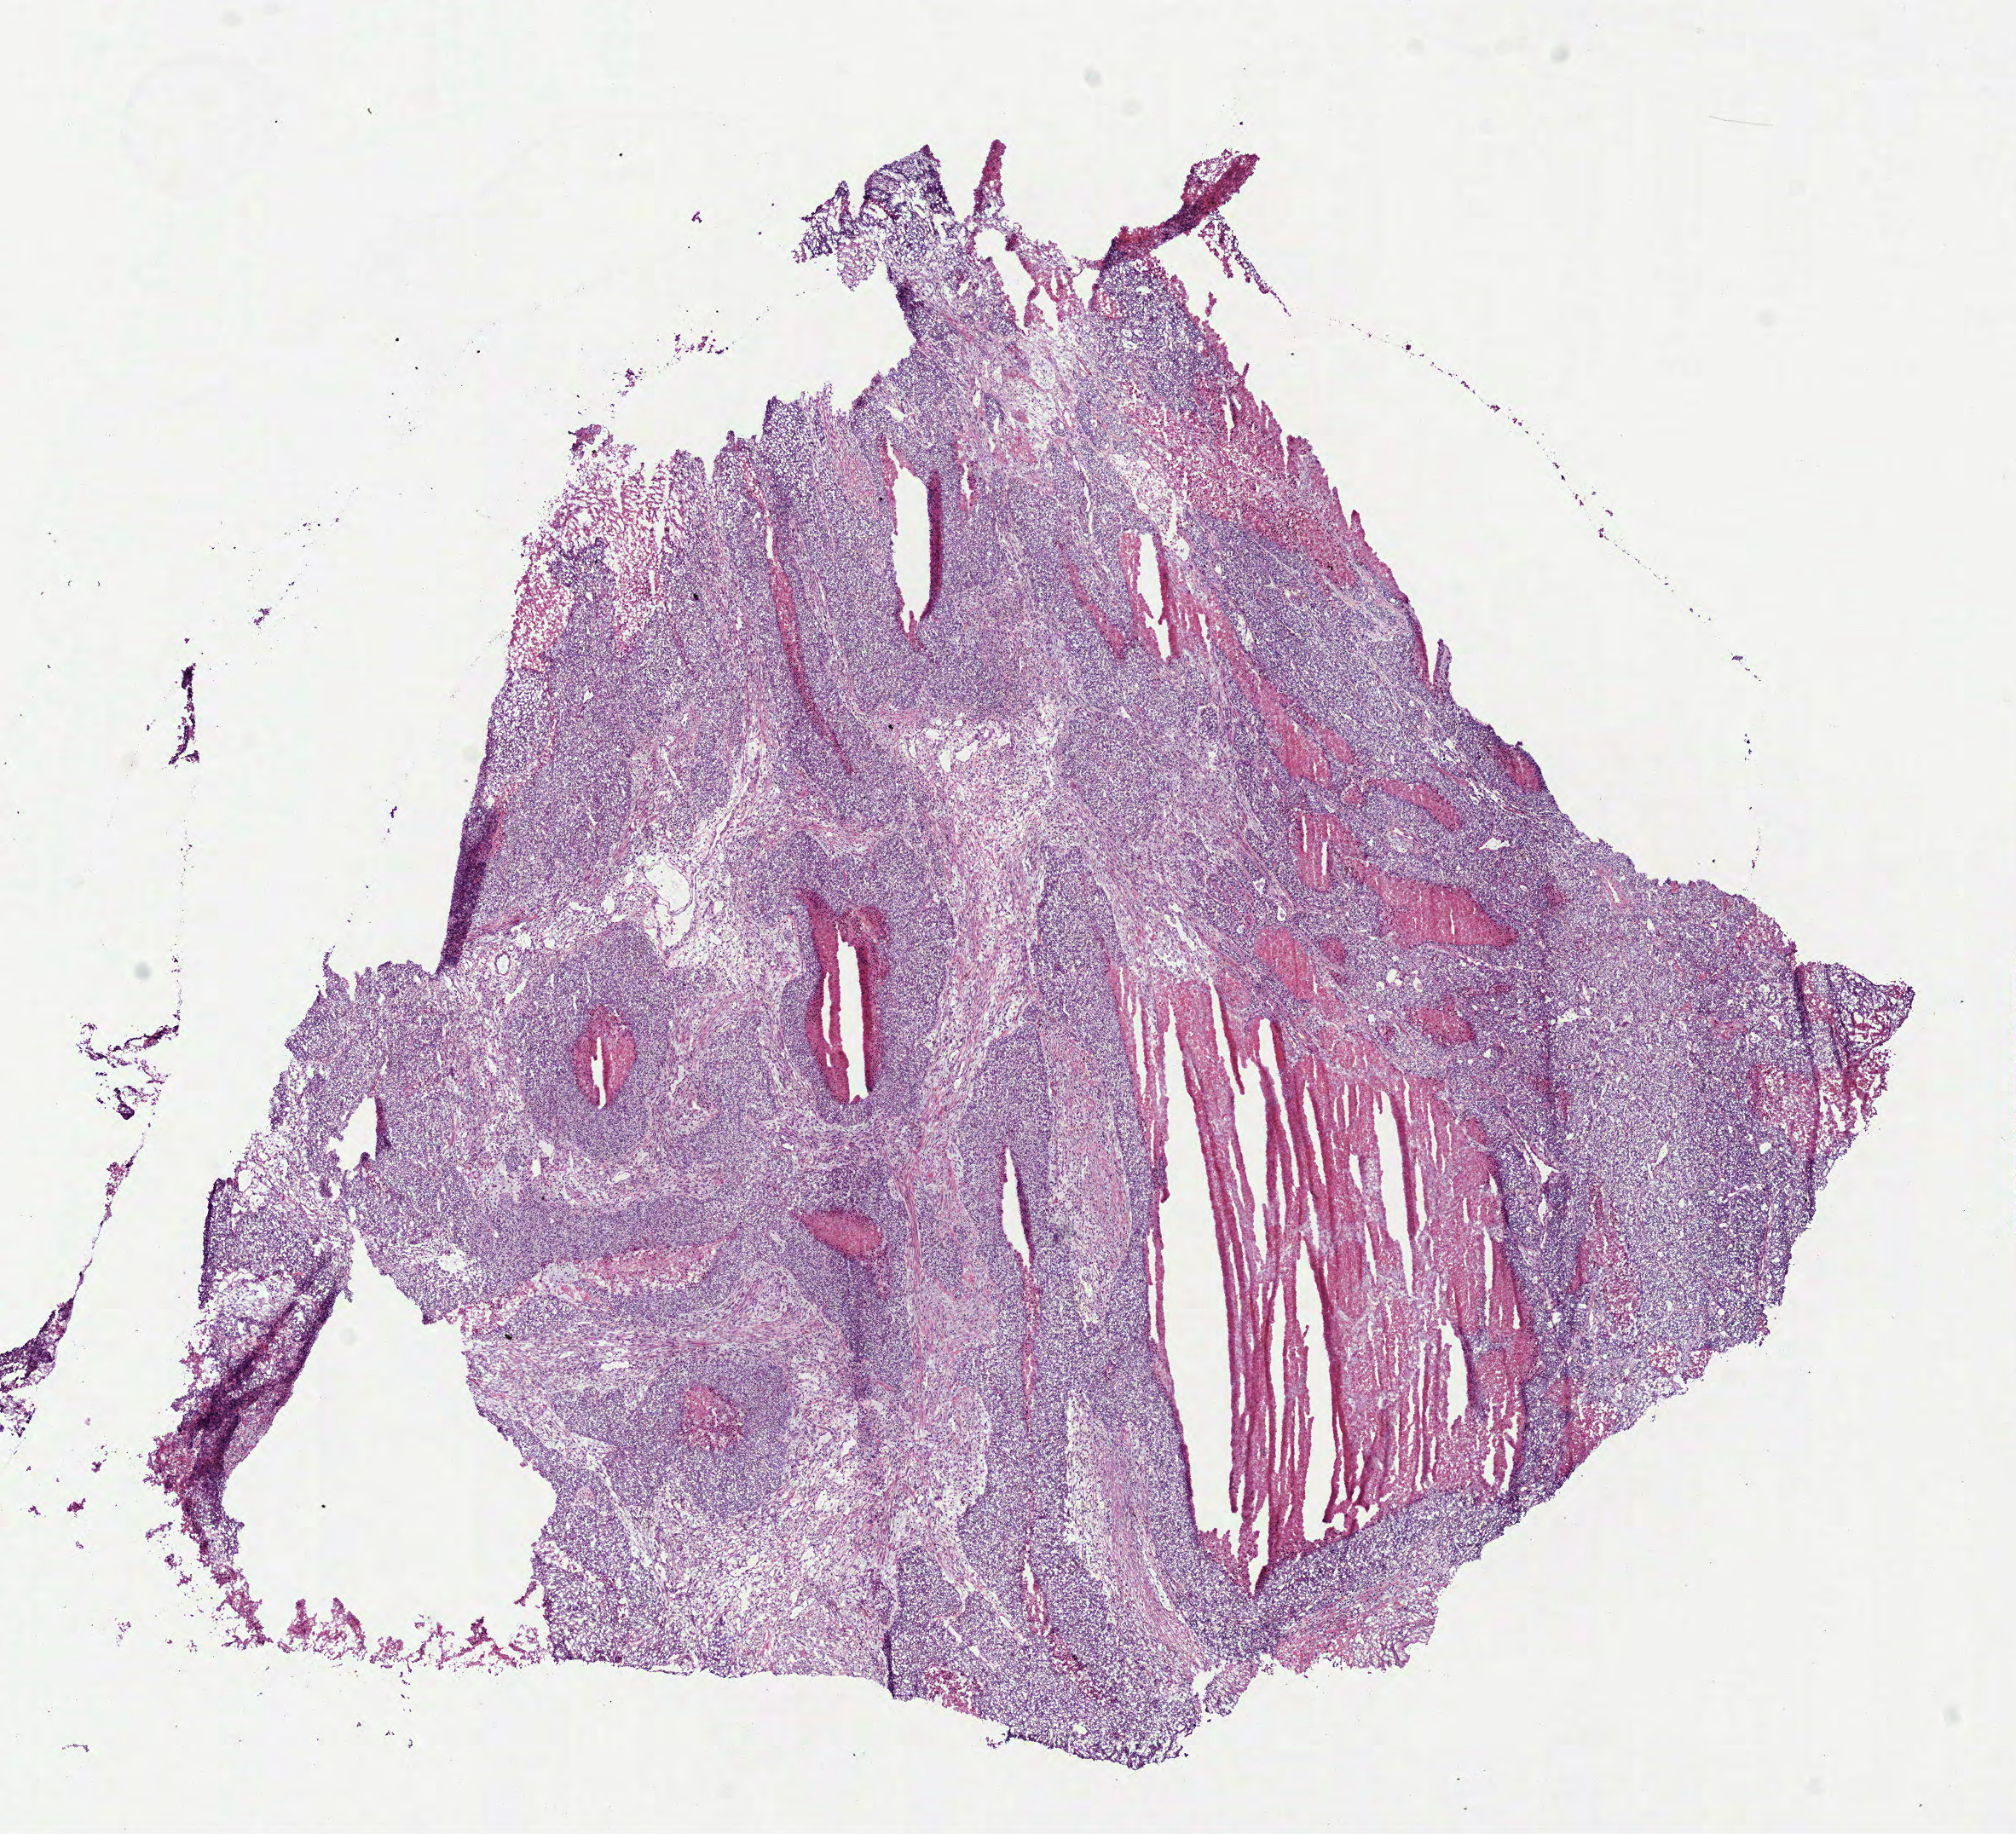
Digitized H&E tissue section (whole slide) — a low-resolution overview of the entire scanned area, about 9.5 x 8.7 mm (from a 40x scan), frozen section from the top of the tissue portion, sample: primary tumour, lung. Female patient; age at initial diagnosis 78 years. Pathologist review of this section (percent, as recorded): tumour cells 80%, tumour nuclei 80%, normal cells 0%, stromal cells 0%, necrosis 20%. Inflammatory infiltration, as recorded: lymphocyte infiltration 10%, monocyte infiltration 0%, neutrophil infiltration 2%.
Pathologic diagnosis: Squamous cell carcinoma, NOS (upper lobe, lung). TNM: T2 N0 M0. AJCC pathologic stage: IB.